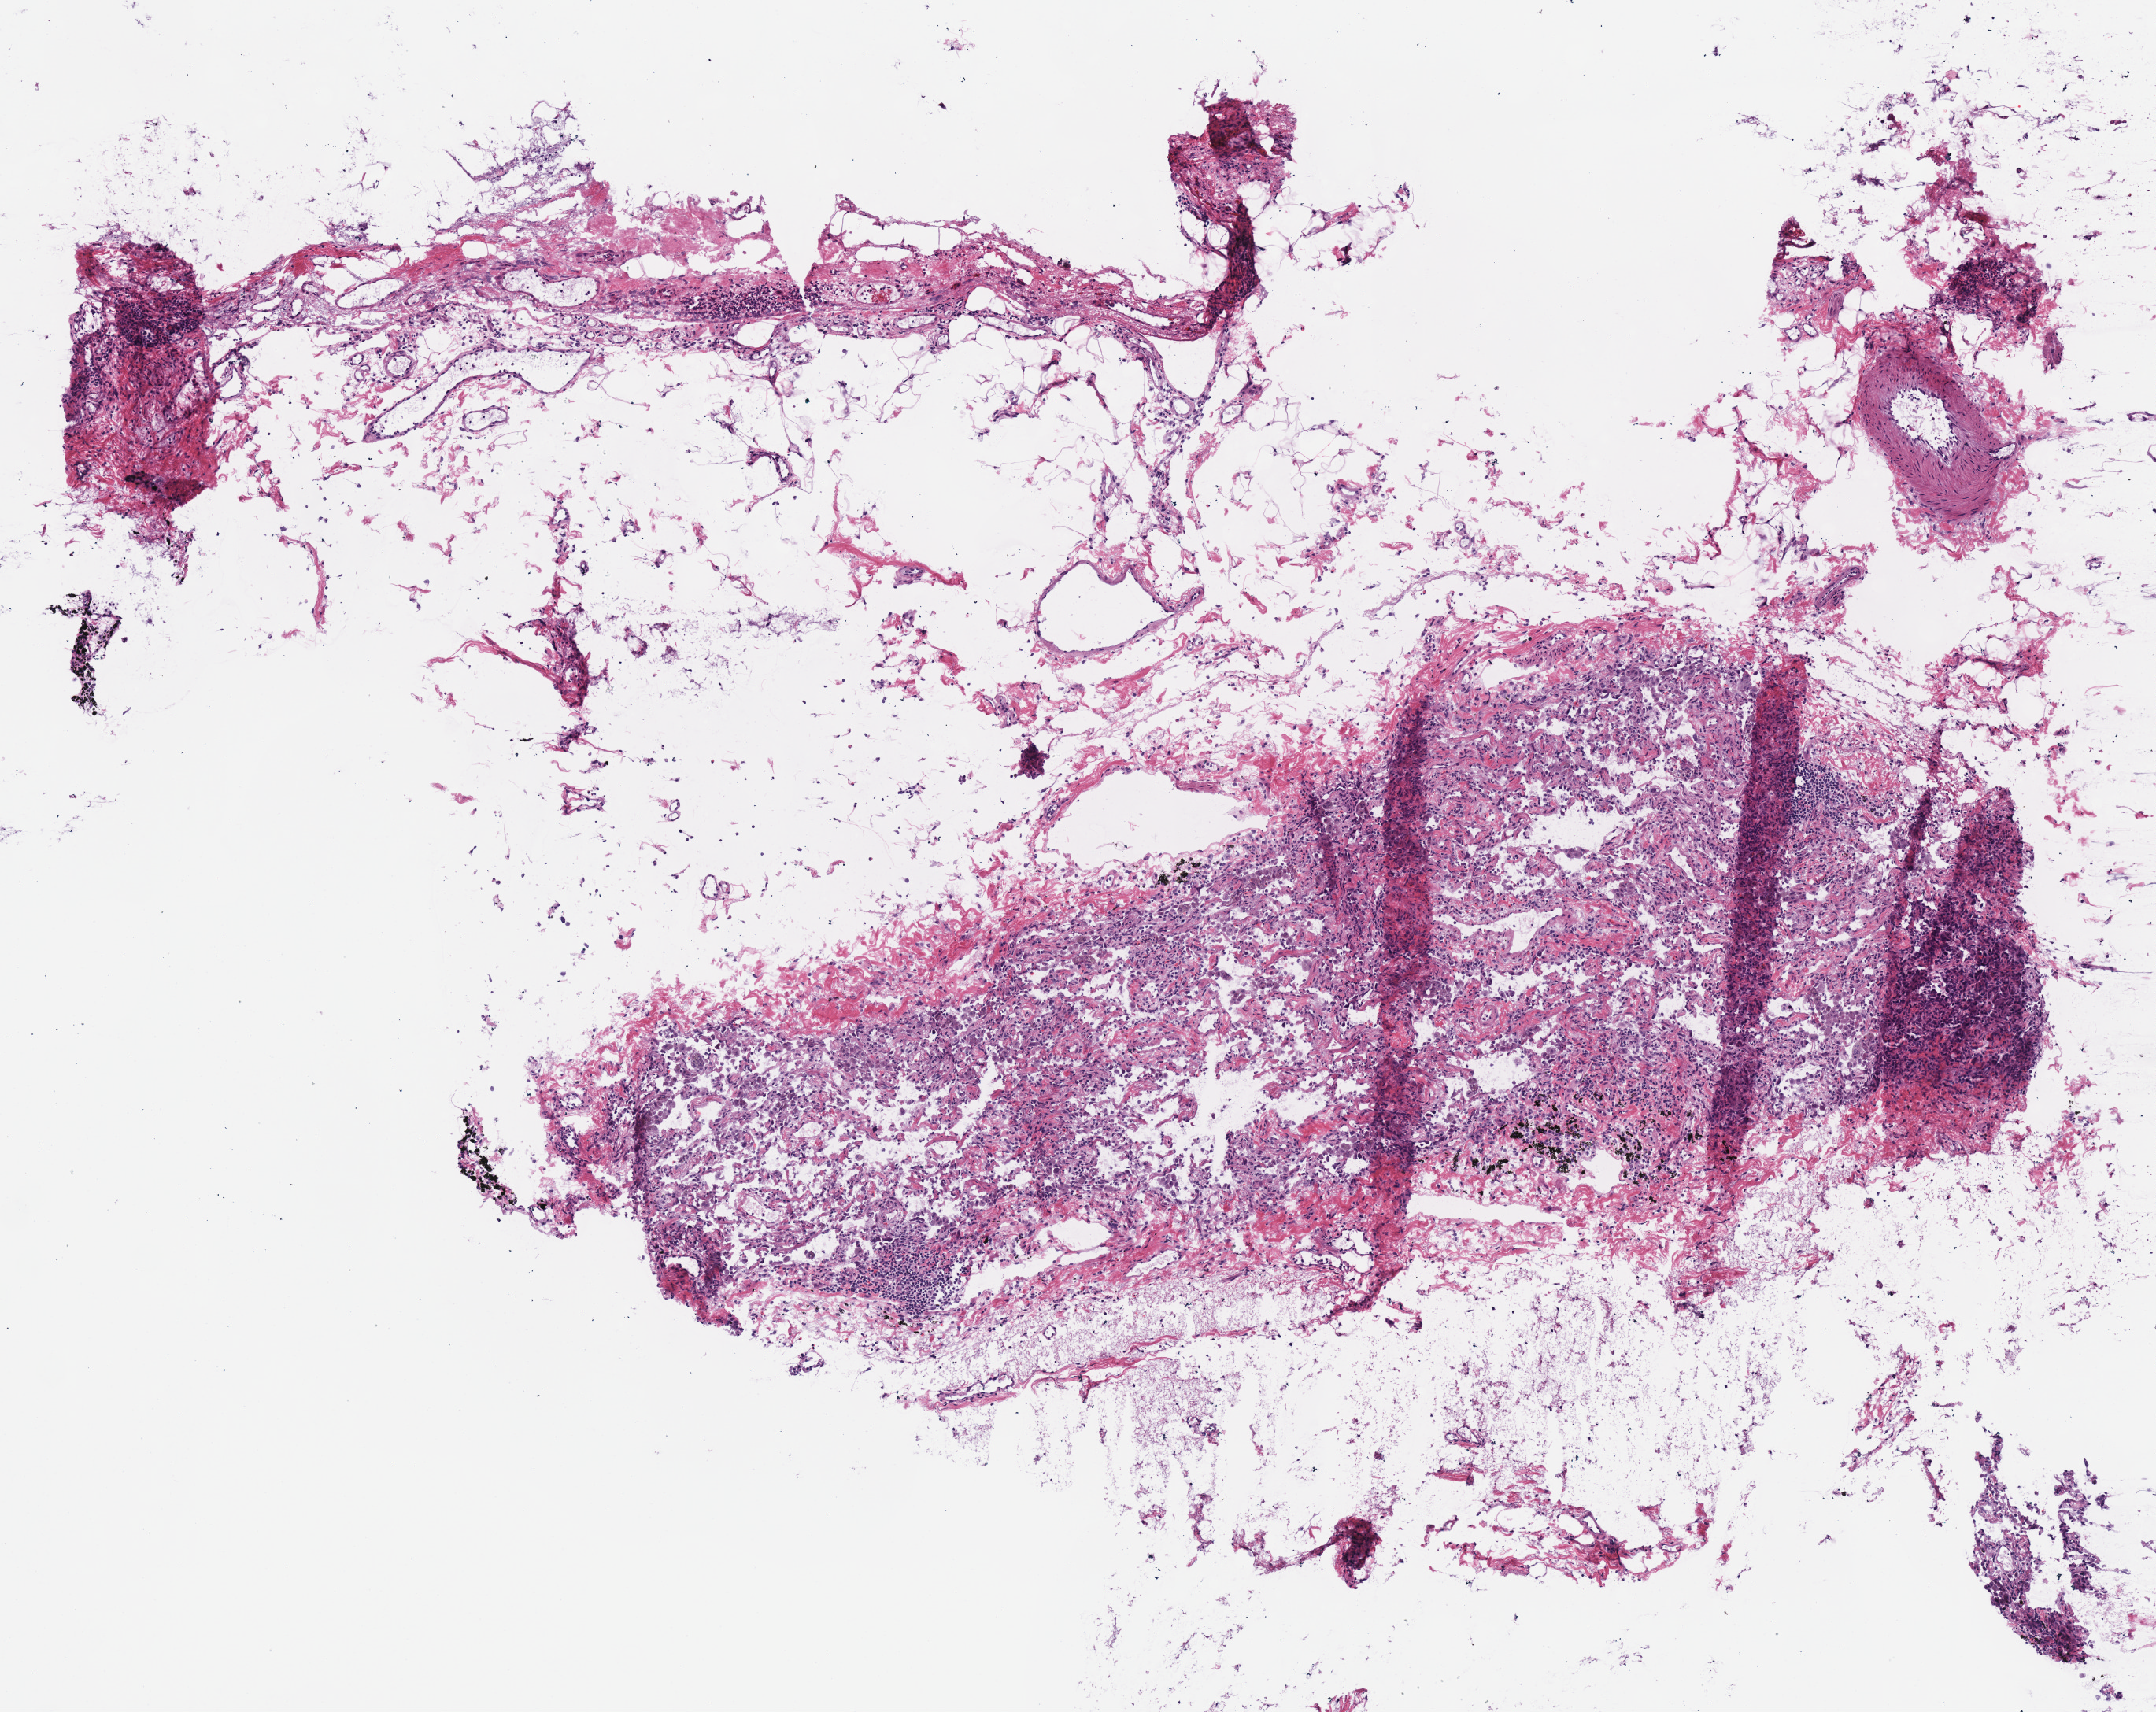
Digitized H&E-stained tissue section (whole slide), whole scanned area (about 5.4 x 4.3 mm, slide scanned at 40x) shown as a low-resolution overview, frozen section from the top of the tissue portion, lung, solid tissue normal (non-tumour tissue) sample. Female patient; age at initial diagnosis 70 years. Infiltration values recorded for this section: lymphocyte infiltration 20%, monocyte infiltration 20%.
* this section: solid tissue normal sample (biorepository sample class)
* patient diagnosis: Adenocarcinoma with mixed subtypes